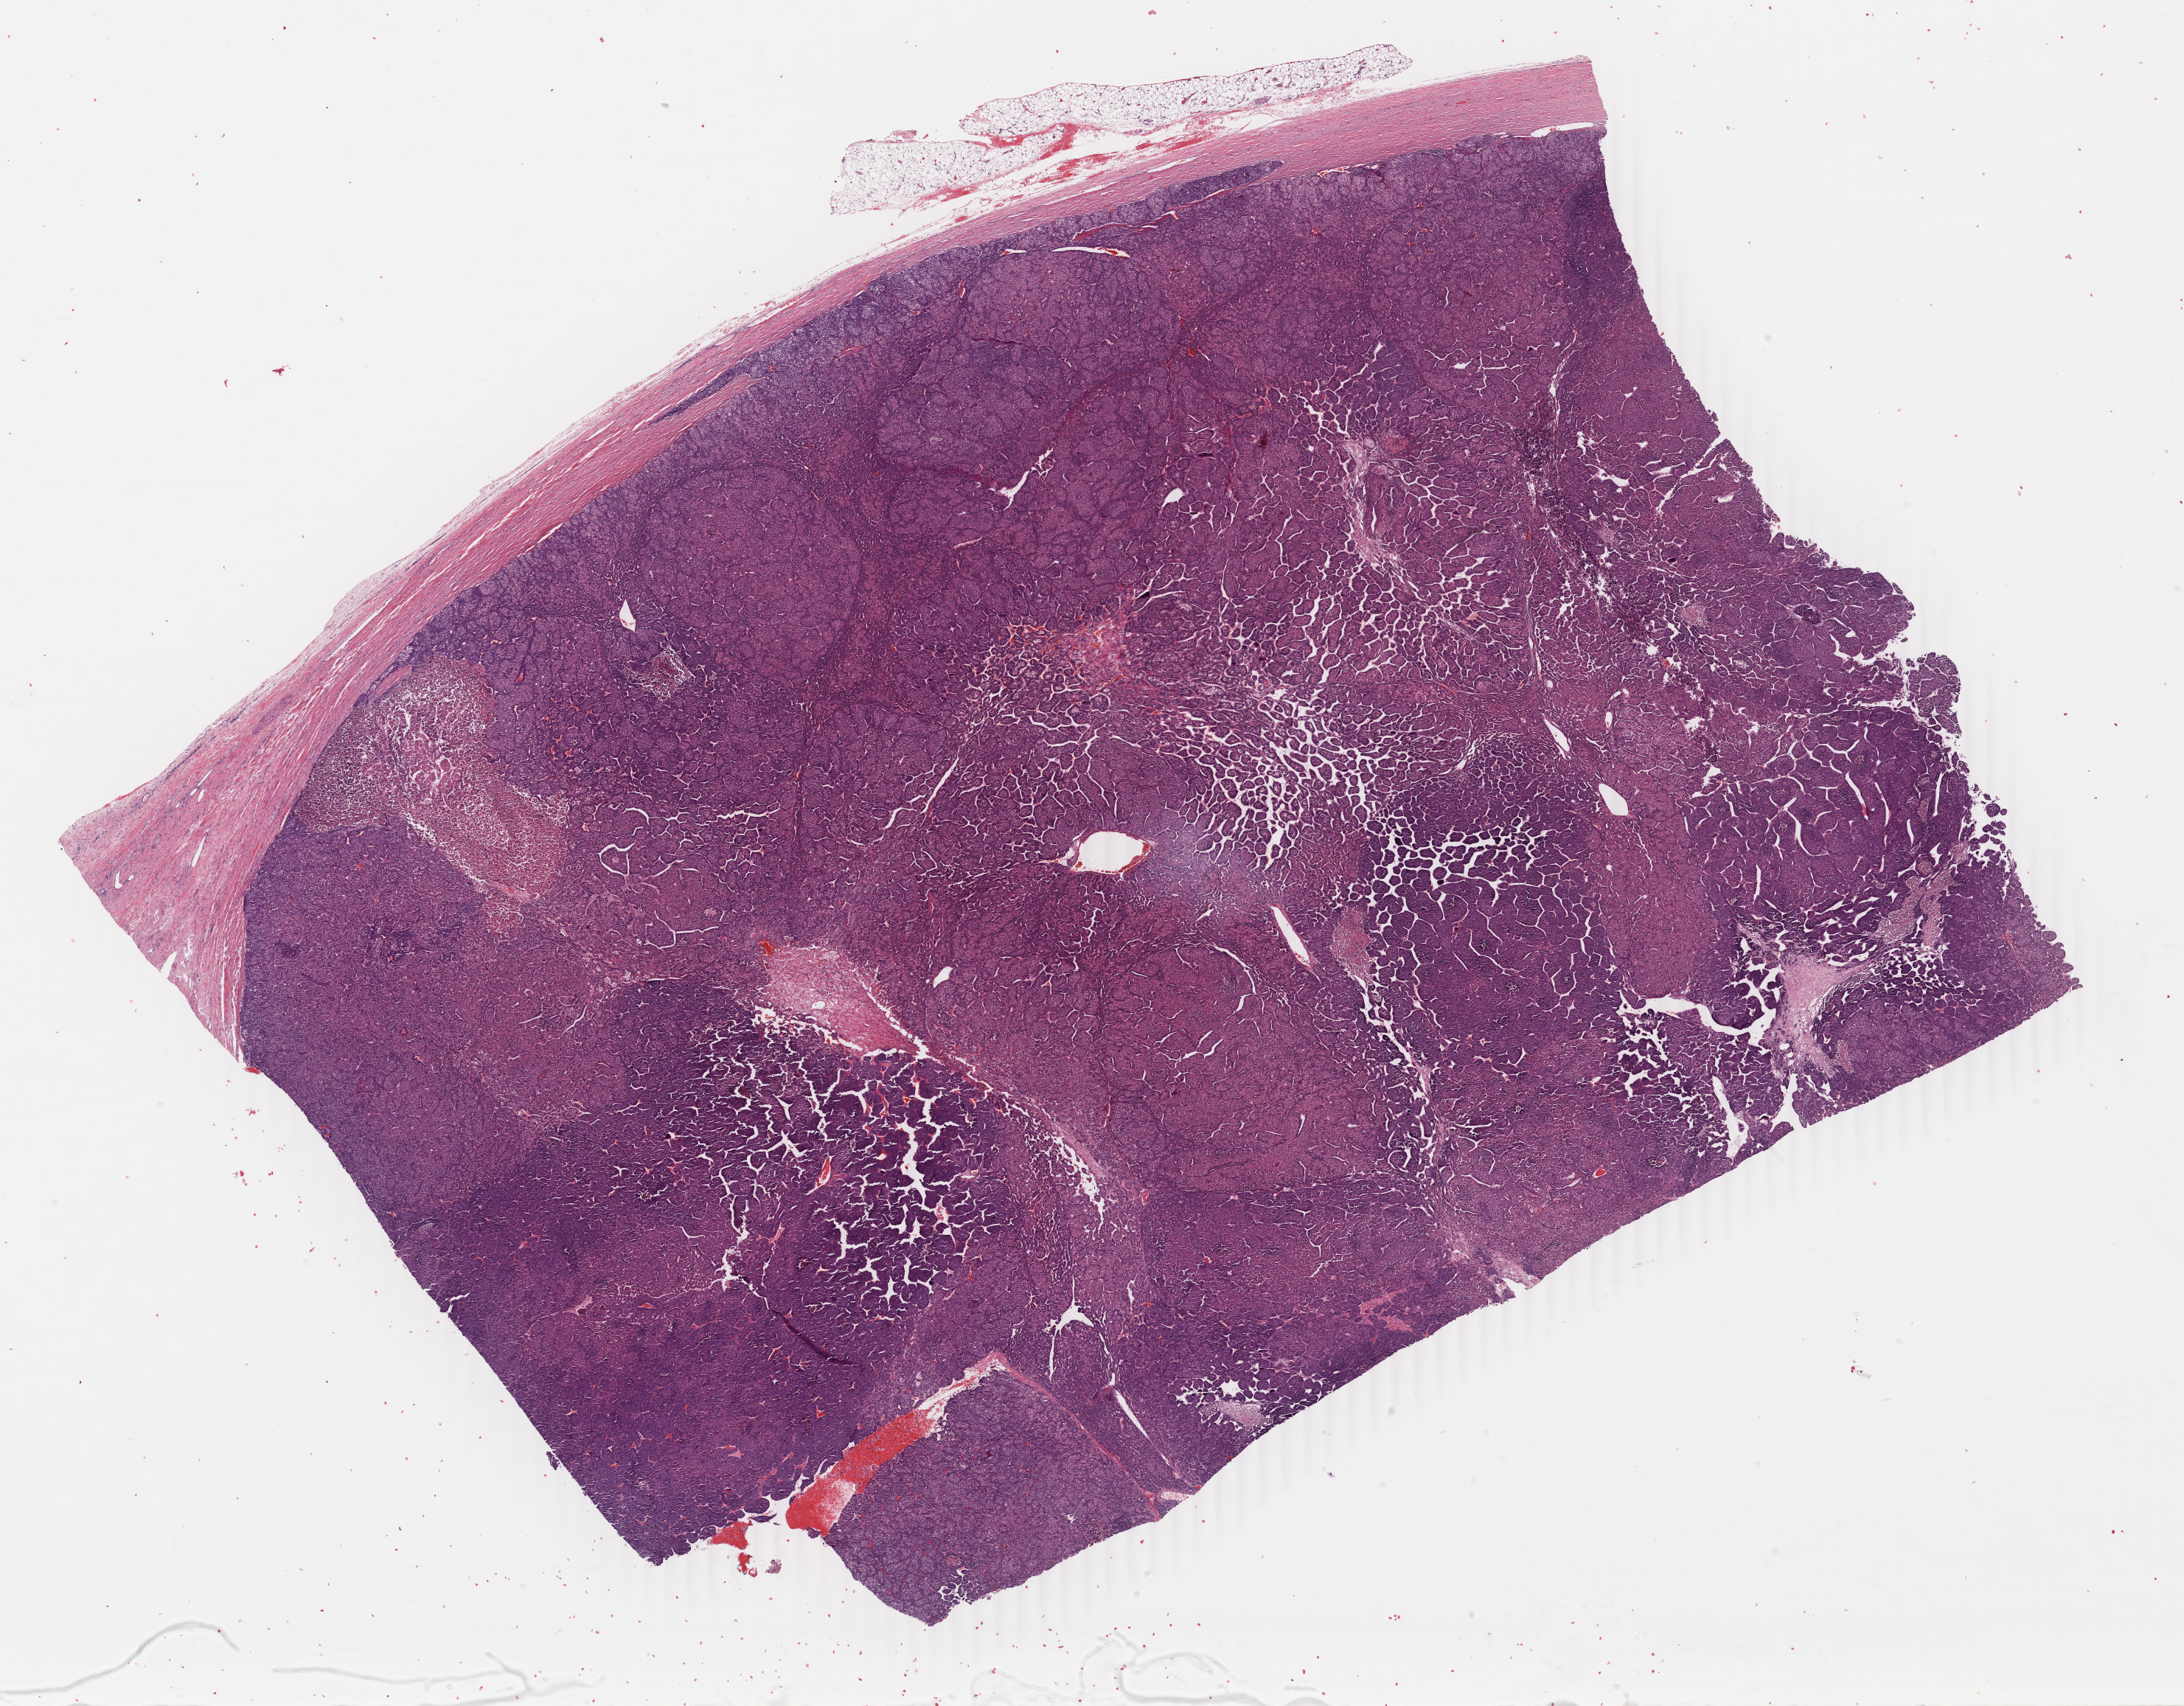
Digitized Hematoxylin and eosin (H&E) stained tissue section (whole slide), low-resolution overview of the scanned area, about 23.6 x 18.4 mm; formalin-fixed paraffin-embedded (FFPE) diagnostic section; sample: primary tumour, liver. Female, age 26 years at initial diagnosis. Histologic grade: G3 (poorly differentiated).
TNM: T2 N0 M1. Pathologic diagnosis: Hepatocellular carcinoma, NOS. AJCC pathologic stage: IV (7th edition).